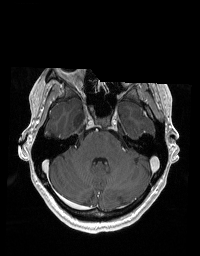
Brain MRI from a brain-tumour surgery series, one axial slice; slice 133 of 192 in the series (ordered by position); T1-weighted post-contrast; 1 mm slice thickness; 200 × 256 image matrix, field of view 195 × 250 mm. From the clinical record (not read from this slice): histopathology: Glioblastoma; WHO grade: 2; IDH mutation: no; tumour location: Right Skull Base Temporal.
Outlined on this slice (outlined manually by an expert reader):
- tumour: box from (x=74, y=107) to (x=85, y=130) px